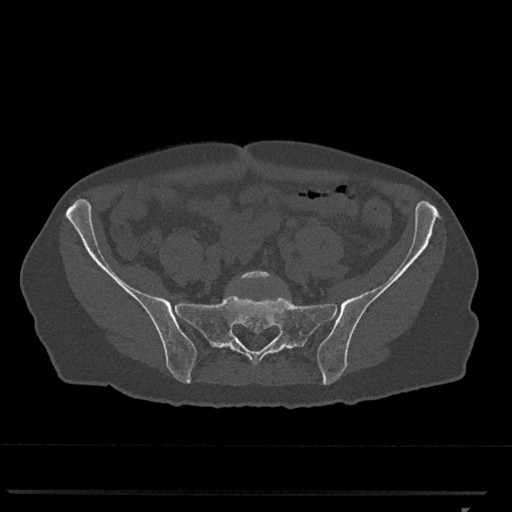
CT including the spine, one axial slice; position 105 of 793 along the scan axis; reconstruction kernel Br40s/3; 120 kVp; bone window (W 1800 / L 400 HU); 512 × 512 image matrix, field of view 380 × 380 mm. Patient: female, 62 years. Case-level facts recorded for this patient, not image findings: primary cancer: renal.
Structures marked on this image (semi-automatically segmented with operator editing):
- L5 vertebra: box from (x=236, y=271) to (x=272, y=282) px